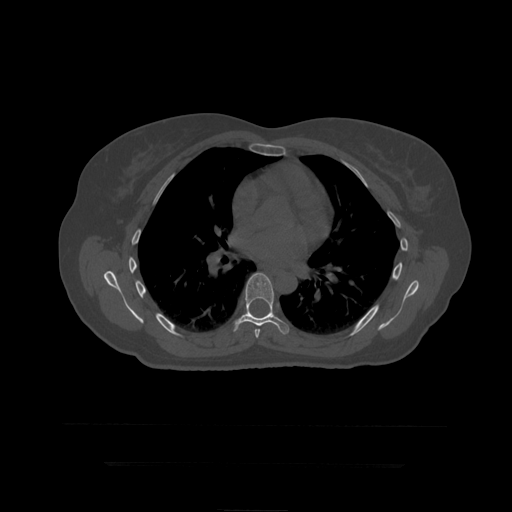
CT including the spine, one axial slice; slice 285 of 399 in the series (ordered by position); 120 kVp; bone window (W 1800 / L 400 HU); 1.25 mm slice thickness; 512 × 512 image matrix, field of view 450 × 450 mm. Patient age 41 years. From the clinical record (not read from this slice): primary cancer: breast.
Outlined on this slice (semi-automatic segmentation, software-assisted and operator-edited):
- T7 vertebra: box from (x=255, y=329) to (x=260, y=339) px
- T8 vertebra: (x=233, y=273)–(x=290, y=335)